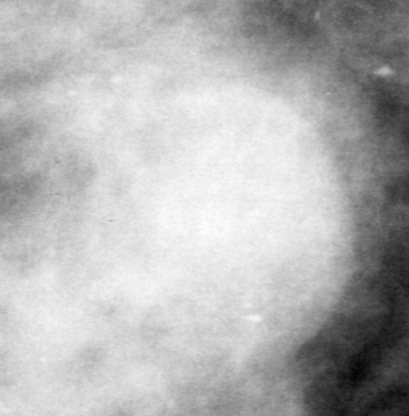
Cropped region of a digitized screen-film mammogram centred on a radiologist-marked abnormality, left breast, MLO view, BI-RADS breast density category 4 (scale 1–4).
Mass, shape round, margins obscured; BI-RADS assessment category 4; subtlety rating 3 on a 1 (subtle) to 5 (obvious) scale; pathology (as recorded): benign.